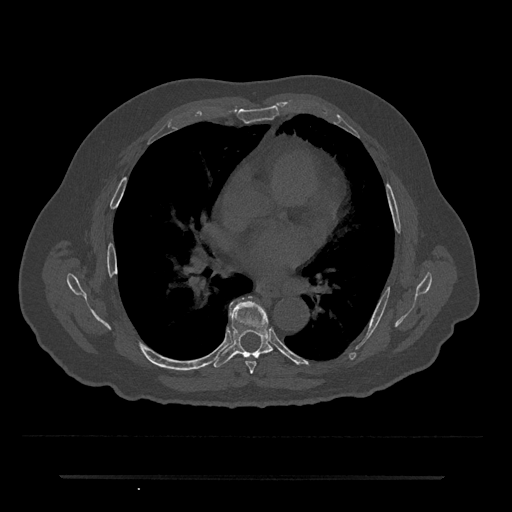
CT including the spine, one axial slice; slice 406 of 797 in the series (ordered by position); reconstruction kernel Br40s/3; 120 kVp; bone window (W 1800 / L 400 HU); 0.5 mm slice thickness; 512 × 512 image matrix, field of view 437 × 437 mm. Patient: male, 69 years. Case-level facts recorded for this patient, not image findings: primary cancer: prostate.
Outlined on this slice (semi-automatically segmented with operator editing):
- T6 vertebra: bounding box [x1, y1, x2, y2] px = [246, 361, 256, 374]
- T7 vertebra: [213, 297, 273, 368]